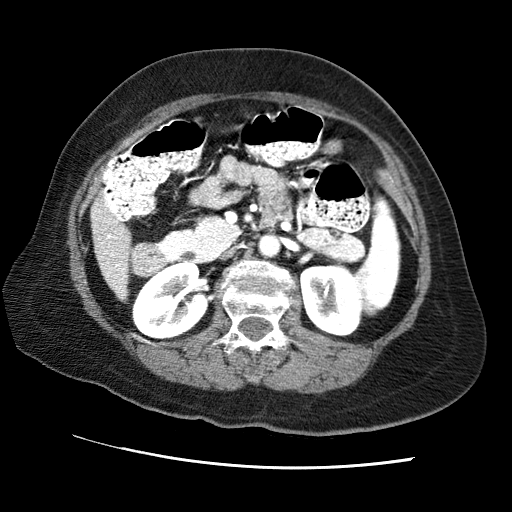
Contrast-enhanced abdominal CT (liver protocol), one axial slice. Position 18 of 65 along the scan axis. Reconstruction kernel STANDARD. Soft-tissue window (W 400 / L 40 HU). 2.5 mm slice thickness. 512 × 512 image matrix. From the clinical record (not read from this slice): diagnosis: hepatocellular carcinoma (patient treated with transarterial chemoembolisation; whether this scan precedes or follows treatment is not stated here); TNM stage (as recorded): Stage-II; Child-Pugh class: A; tumour differentiation: no biopsy.
Structures marked on this image (semi-automatic segmentation, software-assisted and operator-edited):
- liver parenchyma outside the tumour (the mass and vessels are separate outlines, so this box may not span the whole liver): bounding box [x1, y1, x2, y2] px = [90, 196, 130, 299]
- liver vessels: [107, 219, 124, 288]